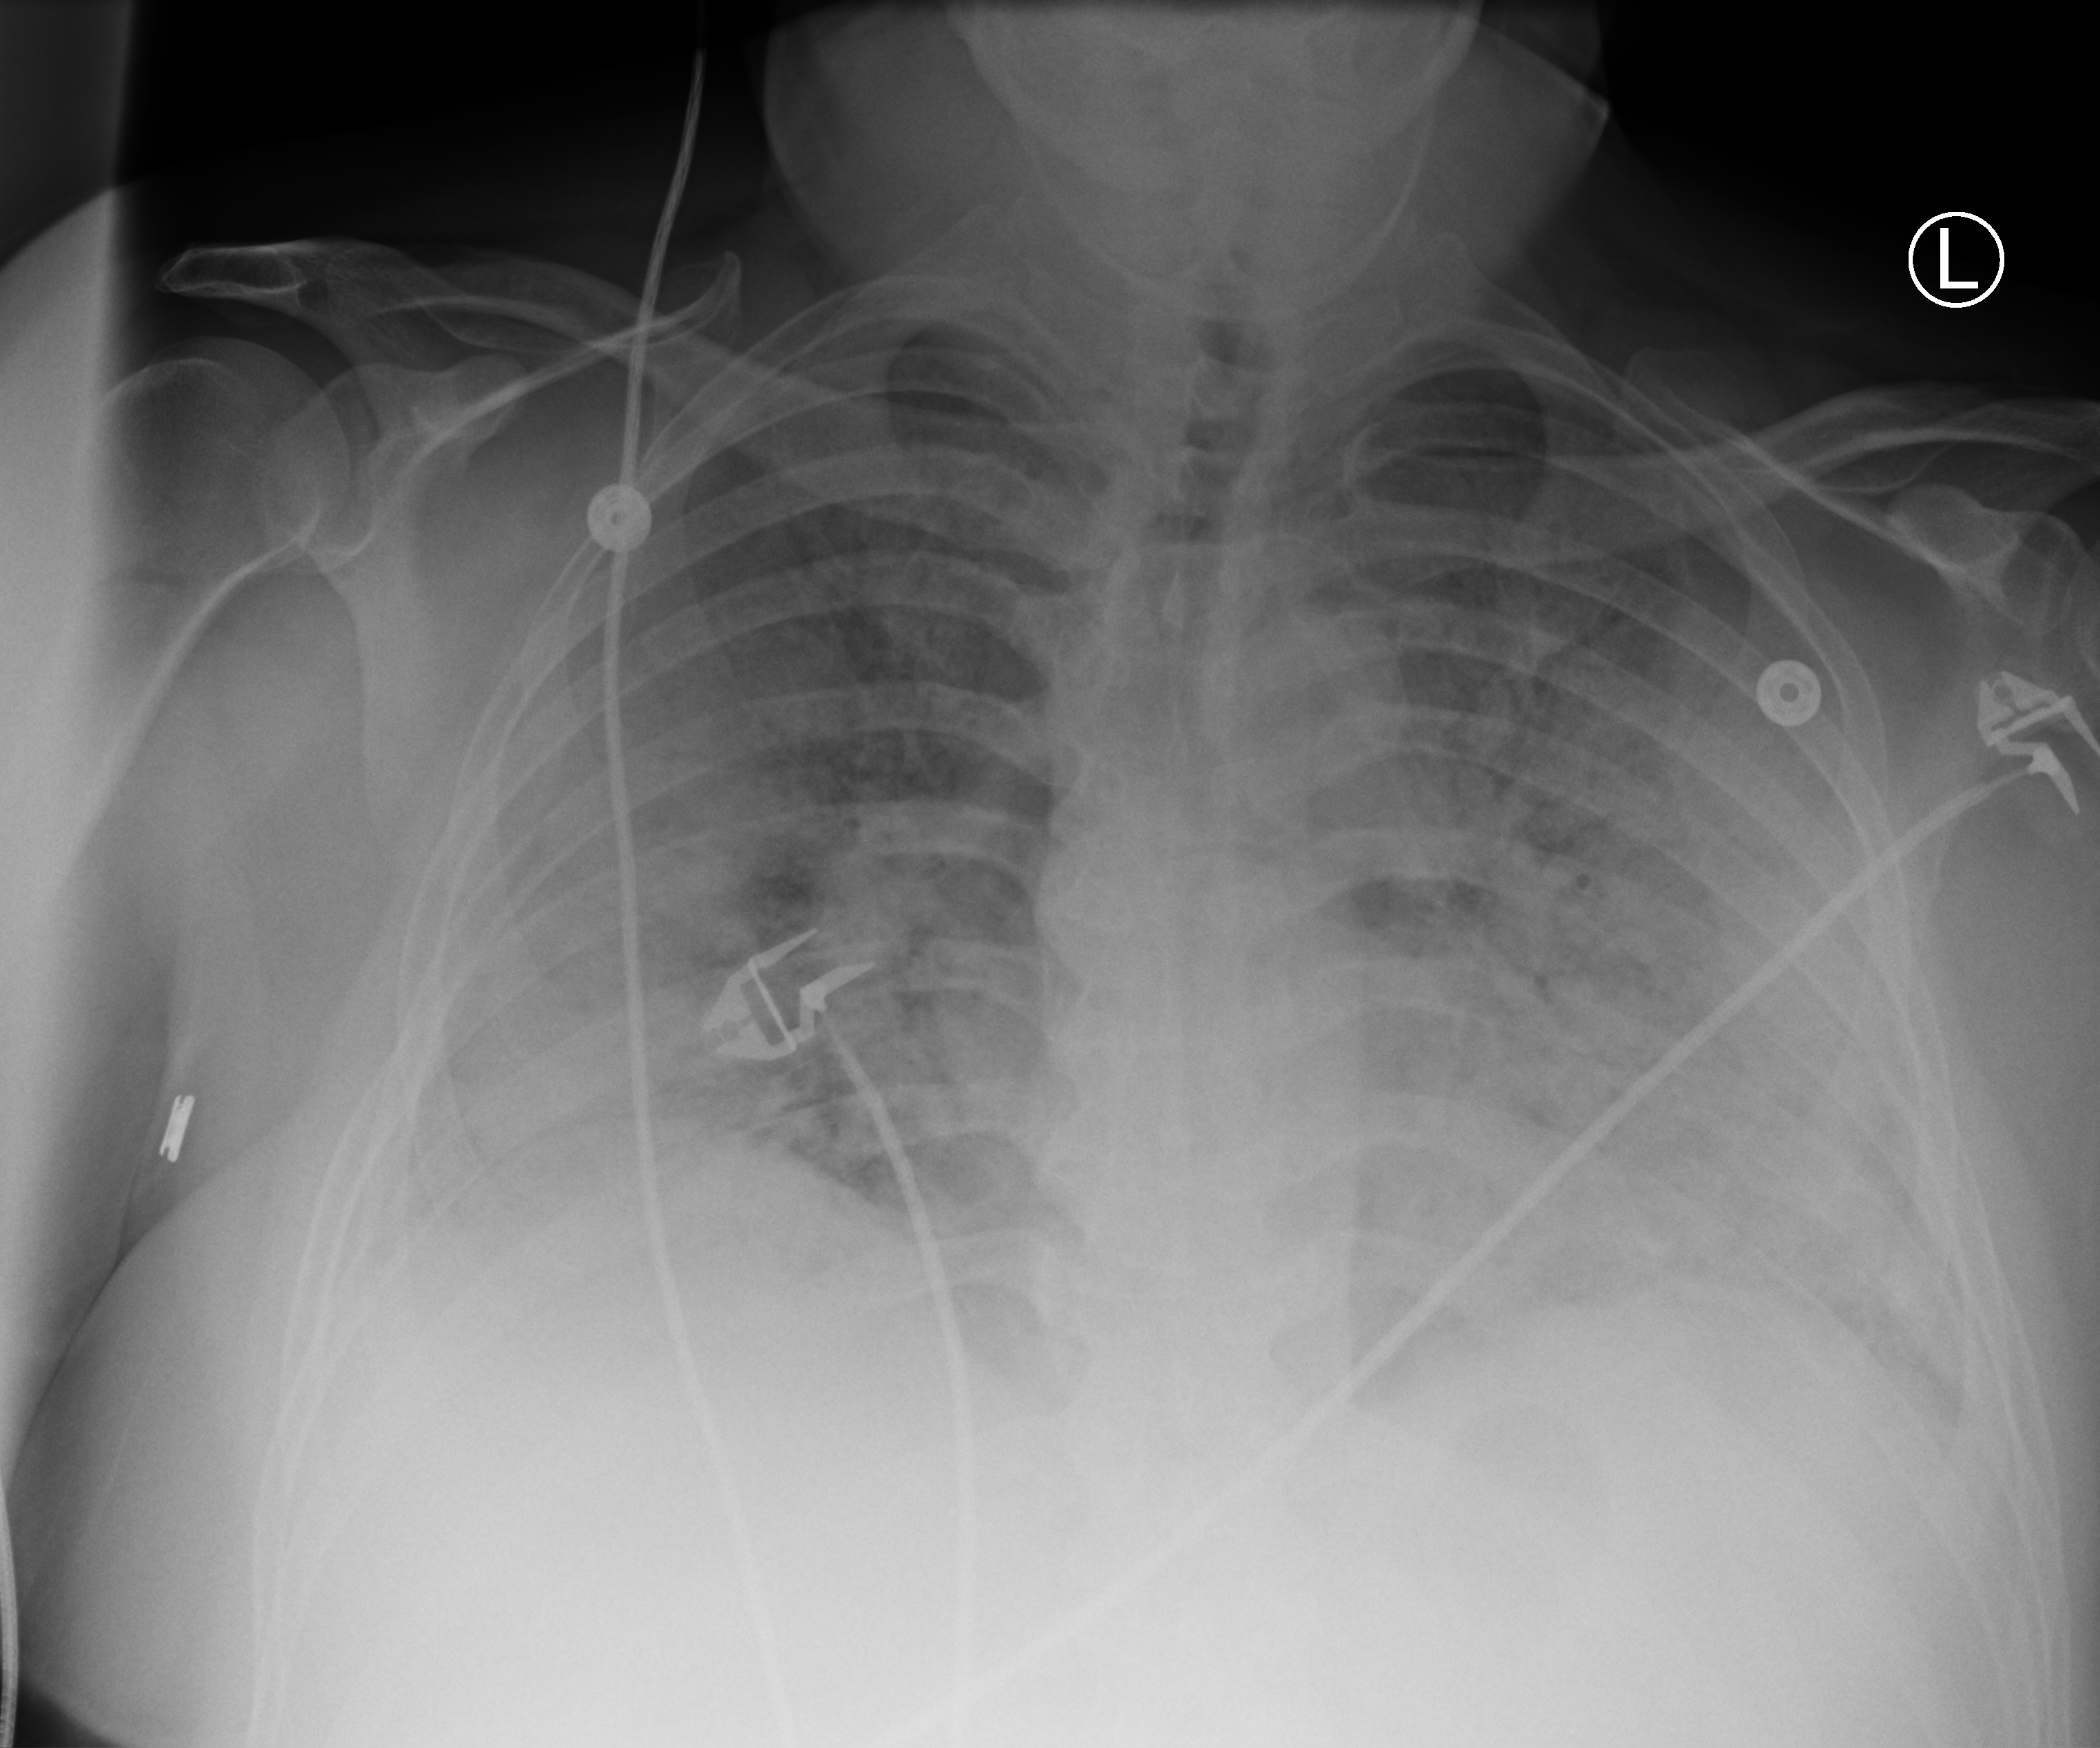
Chest X-ray (portable), anteroposterior (AP) projection. Patient hospitalised with COVID-19; male, aged 18–59 years.
Admission-level facts for this patient (not findings on this image; timing relative to this image not recorded): hypertension (admission record): no.